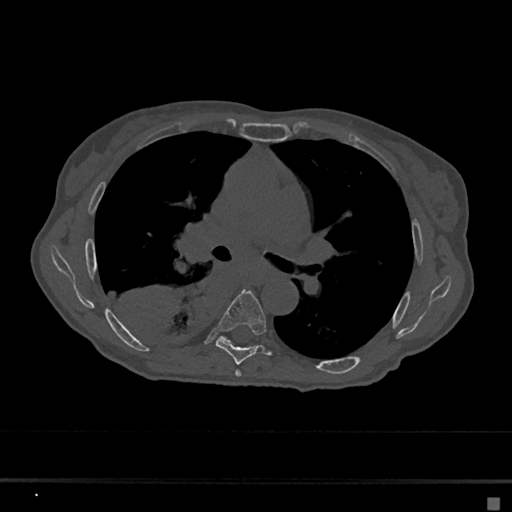
CT including the spine, one axial slice. Slice 414 of 797 in the series (ordered by position). Reconstruction kernel Br40s/3. Bone window (W 1800 / L 400 HU). 0.5 mm slice thickness. 512 × 512 image matrix. Female patient, age 68 years. From the clinical record (not read from this slice): primary cancer: renal.
Annotated regions visible in this slice (semi-automatic segmentation, software-assisted and operator-edited):
- T5 vertebra: bounding box (x1, y1, x2, y2) in pixels: (235, 370, 242, 377)
- T6 vertebra: (215, 290, 272, 365)
- T7 vertebra: (222, 337, 229, 342)